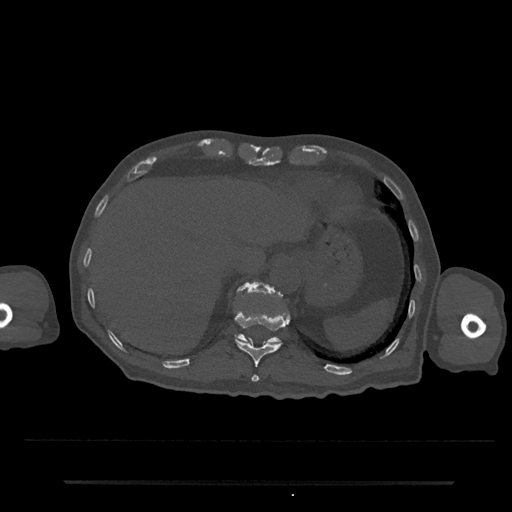
CT including the spine, one axial slice; slice 241 of 797 in the series (ordered by position); reconstruction kernel Br40s/3; bone window (W 1800 / L 400 HU); 0.5 mm slice thickness; 512 × 512 image matrix. Male patient, age 74 years. From the clinical record (not read from this slice): primary cancer: prostate.
Annotated regions visible in this slice (semi-automatic segmentation, software-assisted and operator-edited):
- T11 vertebra: bounding box [x1, y1, x2, y2] px = [234, 311, 289, 382]
- T12 vertebra: [236, 283, 281, 344]